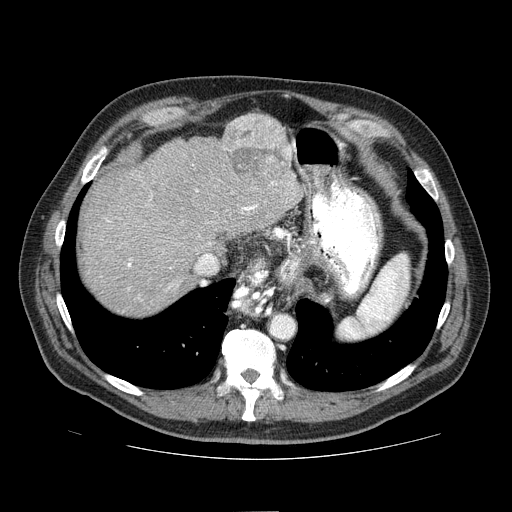
Contrast-enhanced abdominal CT (liver protocol), one axial slice. Position 59 of 81 along the scan axis. Reconstruction kernel STANDARD. 100 kVp. One of 2 acquisitions stored at this slice position. Soft-tissue window (W 400 / L 40 HU). 512 × 512 image matrix, field of view 400 × 400 mm. From the clinical record (not read from this slice): diagnosis: hepatocellular carcinoma (patient treated with transarterial chemoembolisation; whether this scan precedes or follows treatment is not stated here); TNM stage (as recorded): Stage-IIIA; Child-Pugh class: A; tumour nodularity: multinodular.
Structures marked on this image (semi-automatically segmented with operator editing):
- abdominal aorta: box from (x=271, y=315) to (x=294, y=338) px
- liver parenchyma outside the tumour (the mass and vessels are separate outlines, so this box may not span the whole liver): (x=82, y=124)–(x=302, y=316)
- mass: (x=221, y=112)–(x=292, y=185)
- liver vessels: (x=107, y=175)–(x=295, y=290)